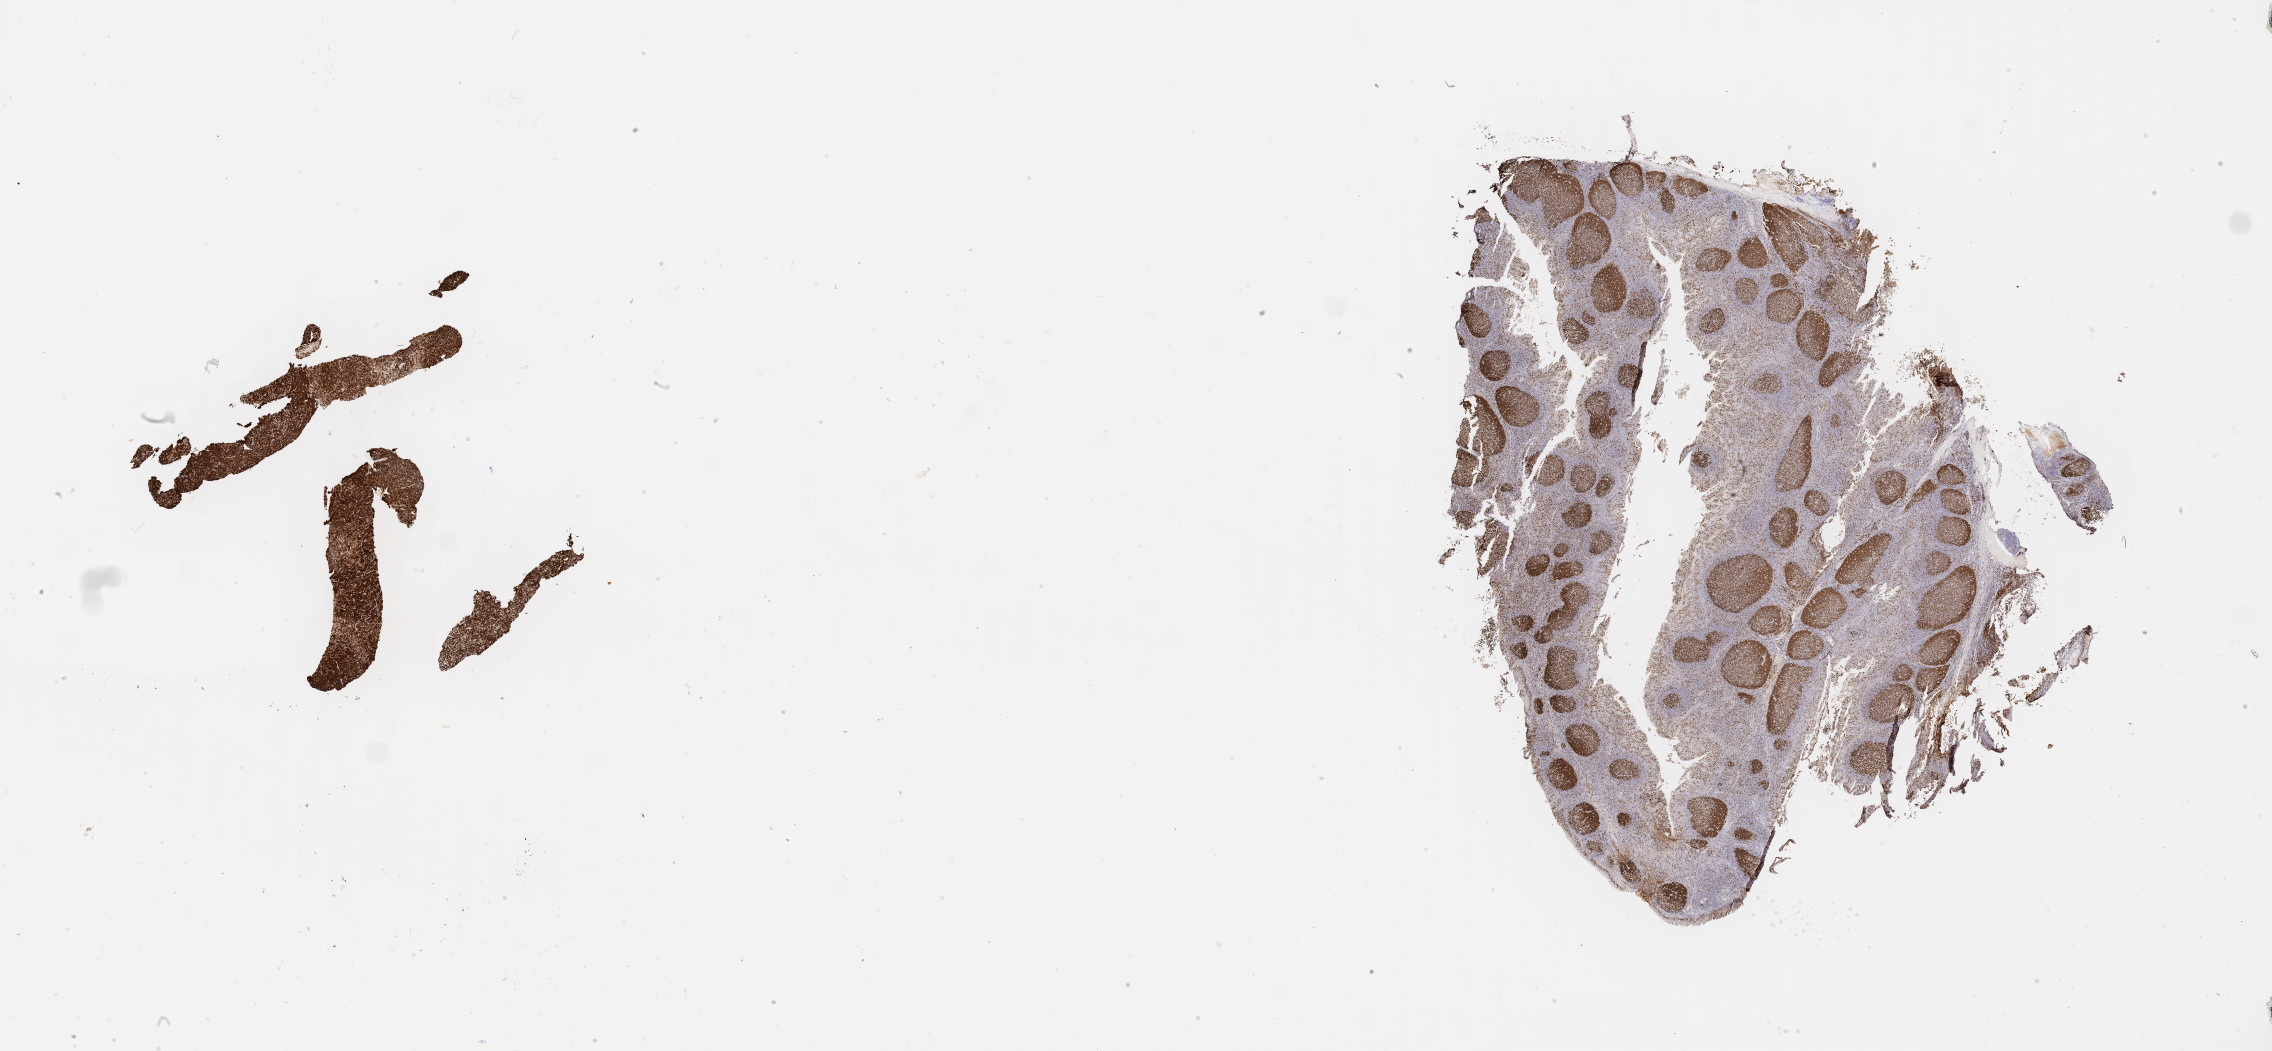
IHC for Ki-67, whole-slide image, shown as a low-resolution overview of the whole scanned area (about 36.7 x 17.0 mm); tumor tissue; anatomic site: abdomen proper. Male patient; age at initial diagnosis 2 years.
Histologic diagnosis: Diffuse large B-cell lymphoma, NOS.